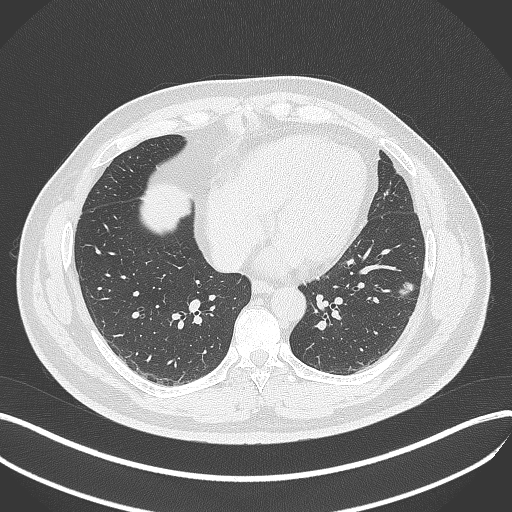
Chest CT, one axial slice; slice 154 of 429 in the series (ordered by position); lung window (W 1500 / L -600 HU); 1 mm slice thickness; 512 × 512 image matrix, field of view 400 × 400 mm. Patient: male, 39 years. From the clinical record (not read from this slice): clinical TNM (as recorded): T2a N0 M0; histopathological grade: G2-3.
Annotated regions visible in this slice (bounding box drawn by a radiologist):
- lung tumour (recorded histology: adenocarcinoma): box from (x=393, y=275) to (x=419, y=306) px